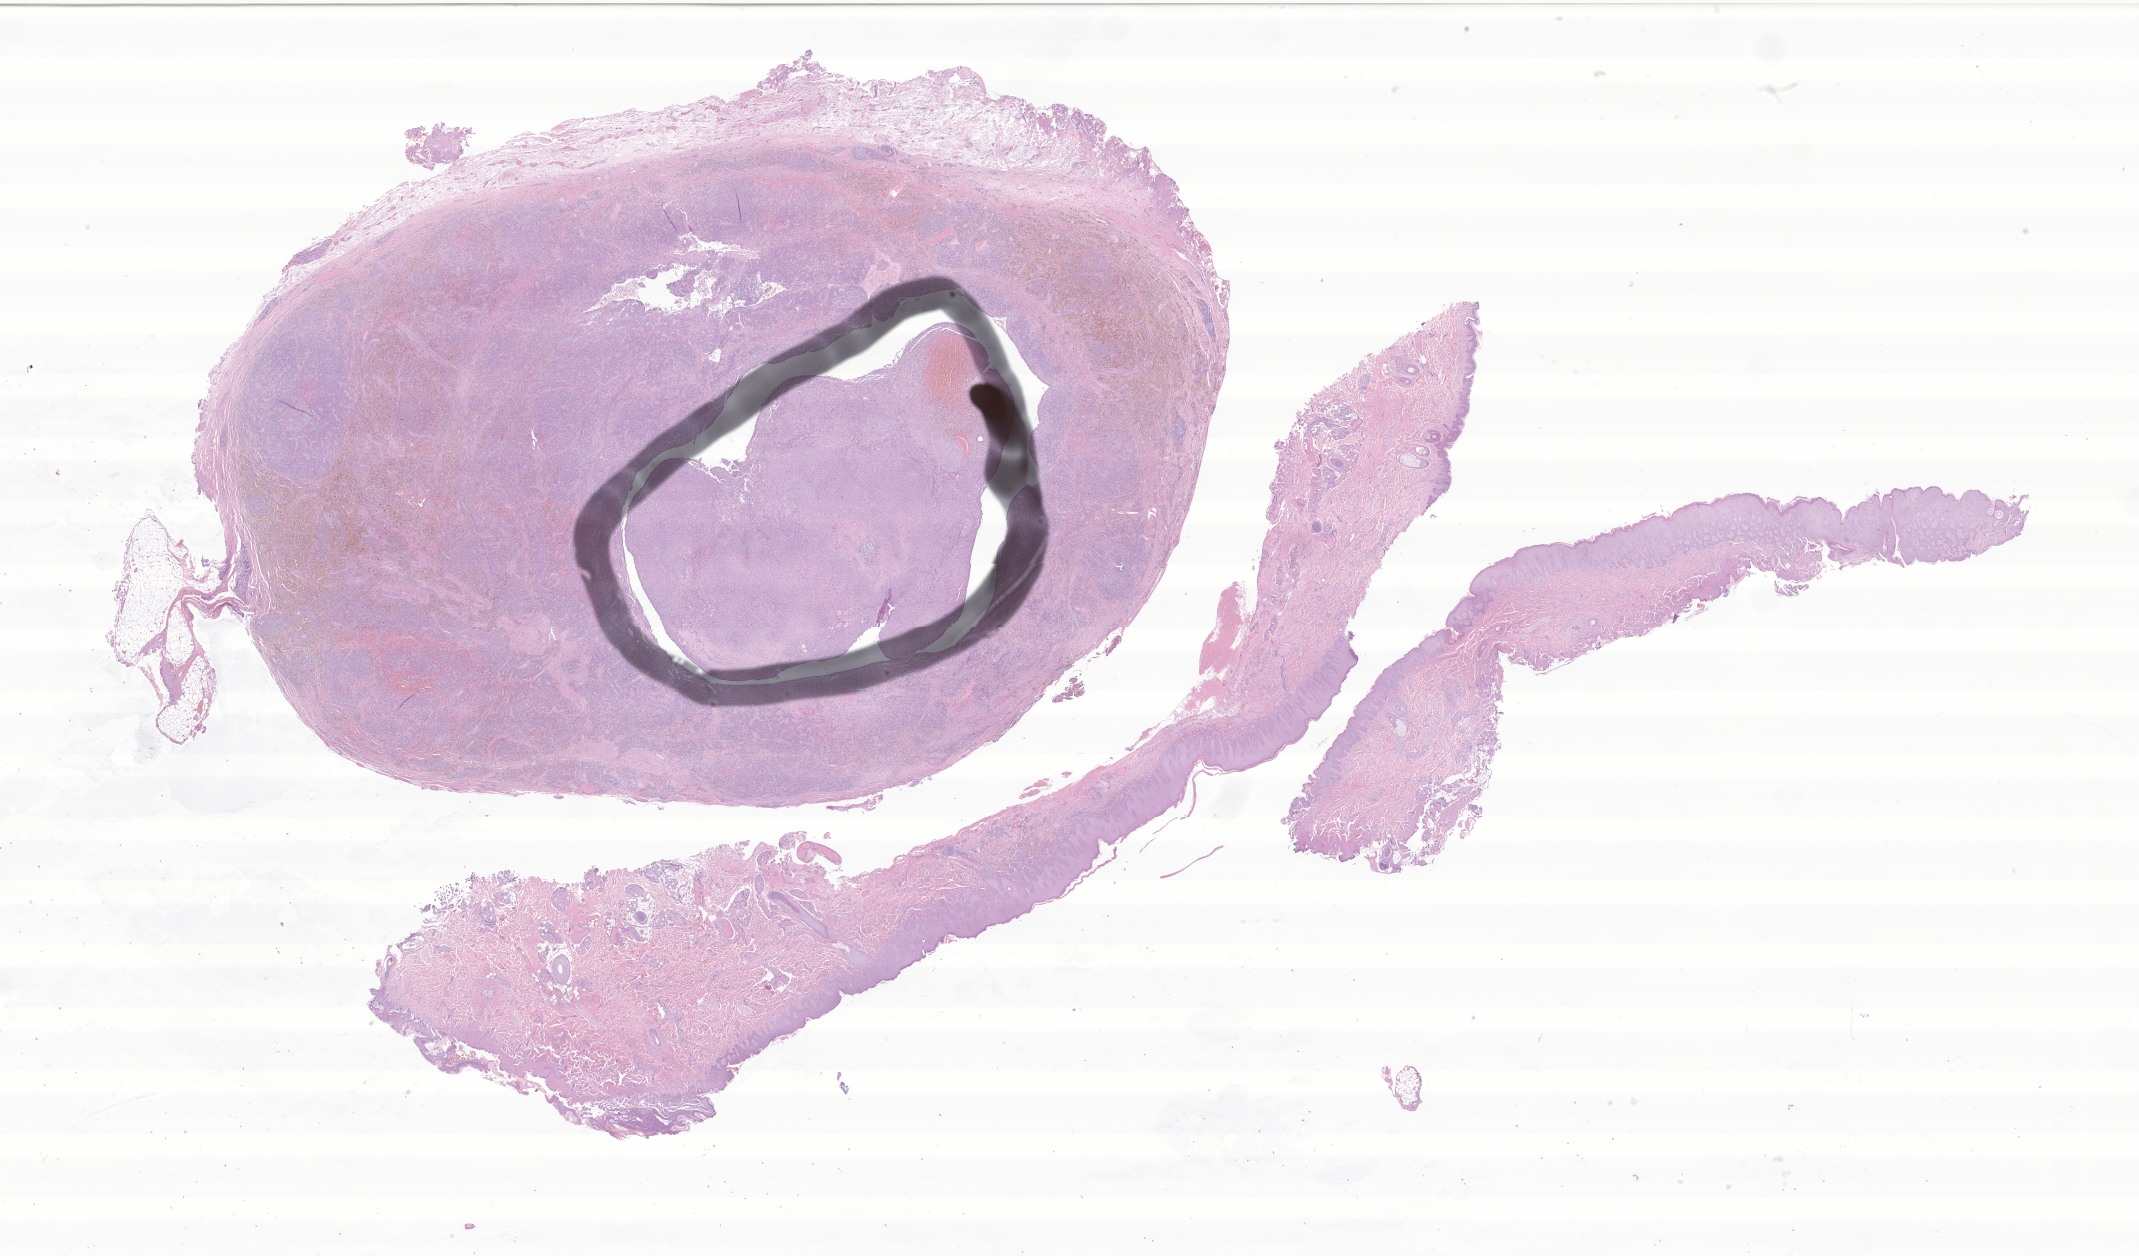
Digitized haematoxylin and eosin-stained section of tumor tissue from the soft tissue of upper extremity — shown as a low-resolution overview of the whole scanned area (about 36.1 x 21.2 mm). Formalin-fixed paraffin-embedded section. Patient: female, age 139 months.
Tissue or organ of origin (case record): connective, subcutaneous and other soft tissues of upper limb and shoulder. Diagnosis: Angiomatoid fibrous histiocytoma.